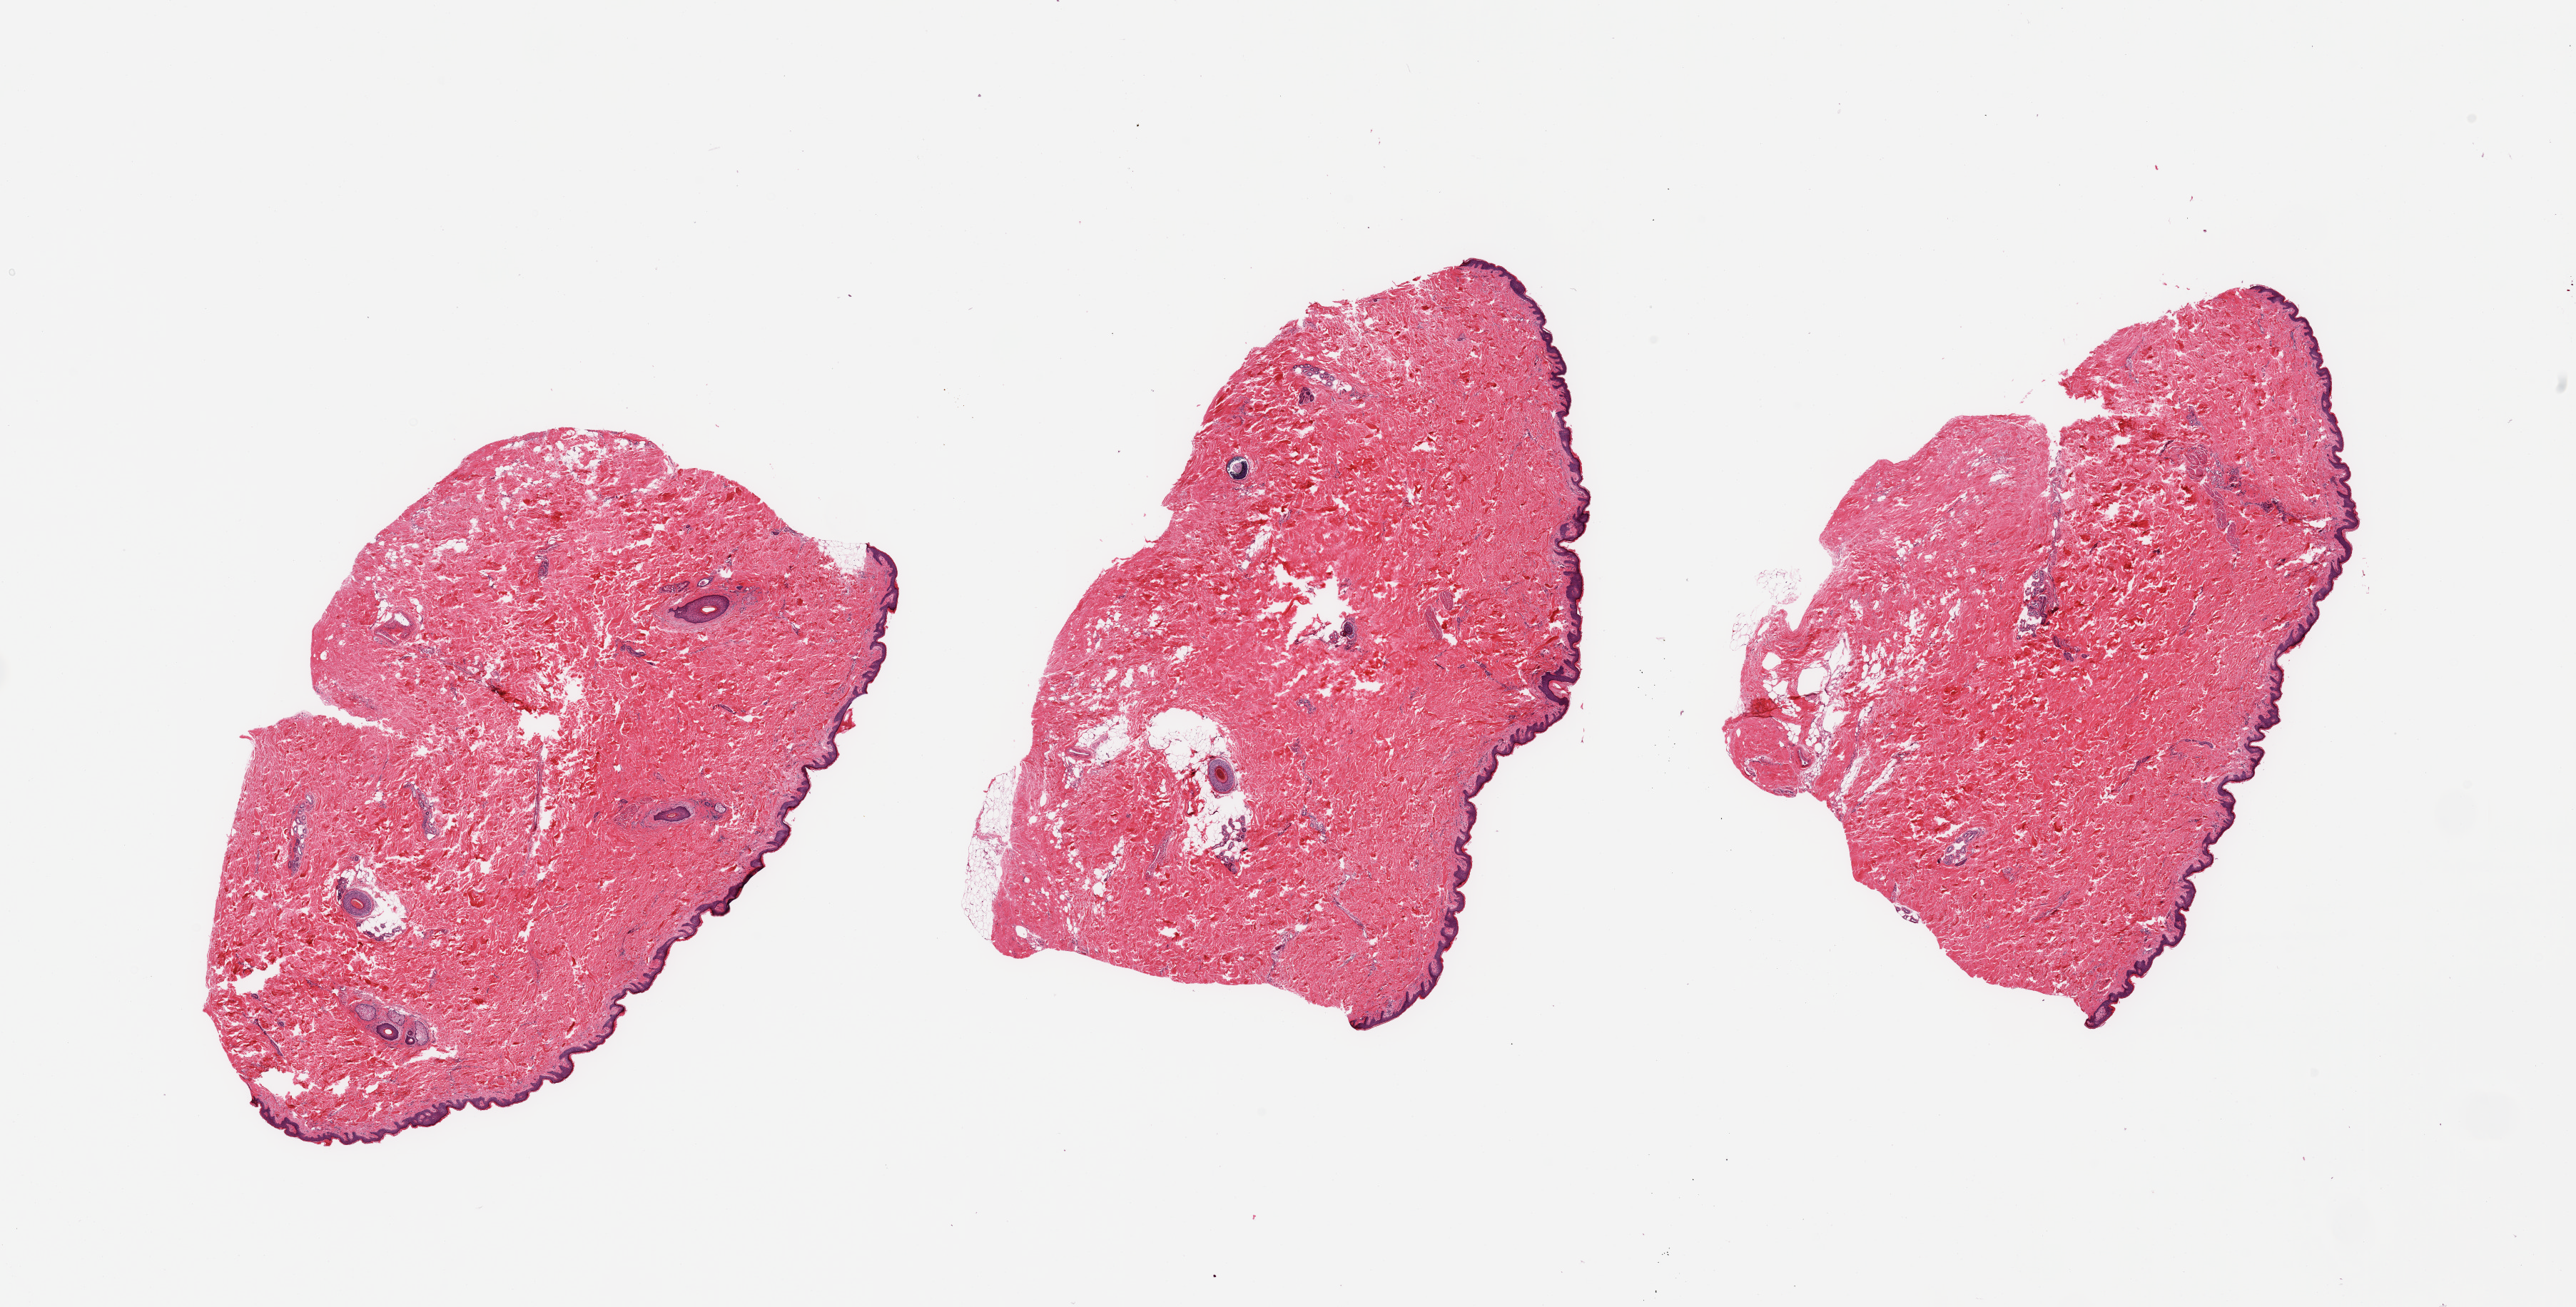
Whole-slide image, hematoxylin and eosin (H&E) stain, low-resolution overview of the scanned area, about 28.5 x 14.5 mm. PAXgene-fixed paraffin-embedded (PFPE) section. Target tissue: skin of suprapubic region. Tissue donor sample. Donor sex: male.
Review note (as recorded): 3 pieces; well trimmed; several hair follicles.